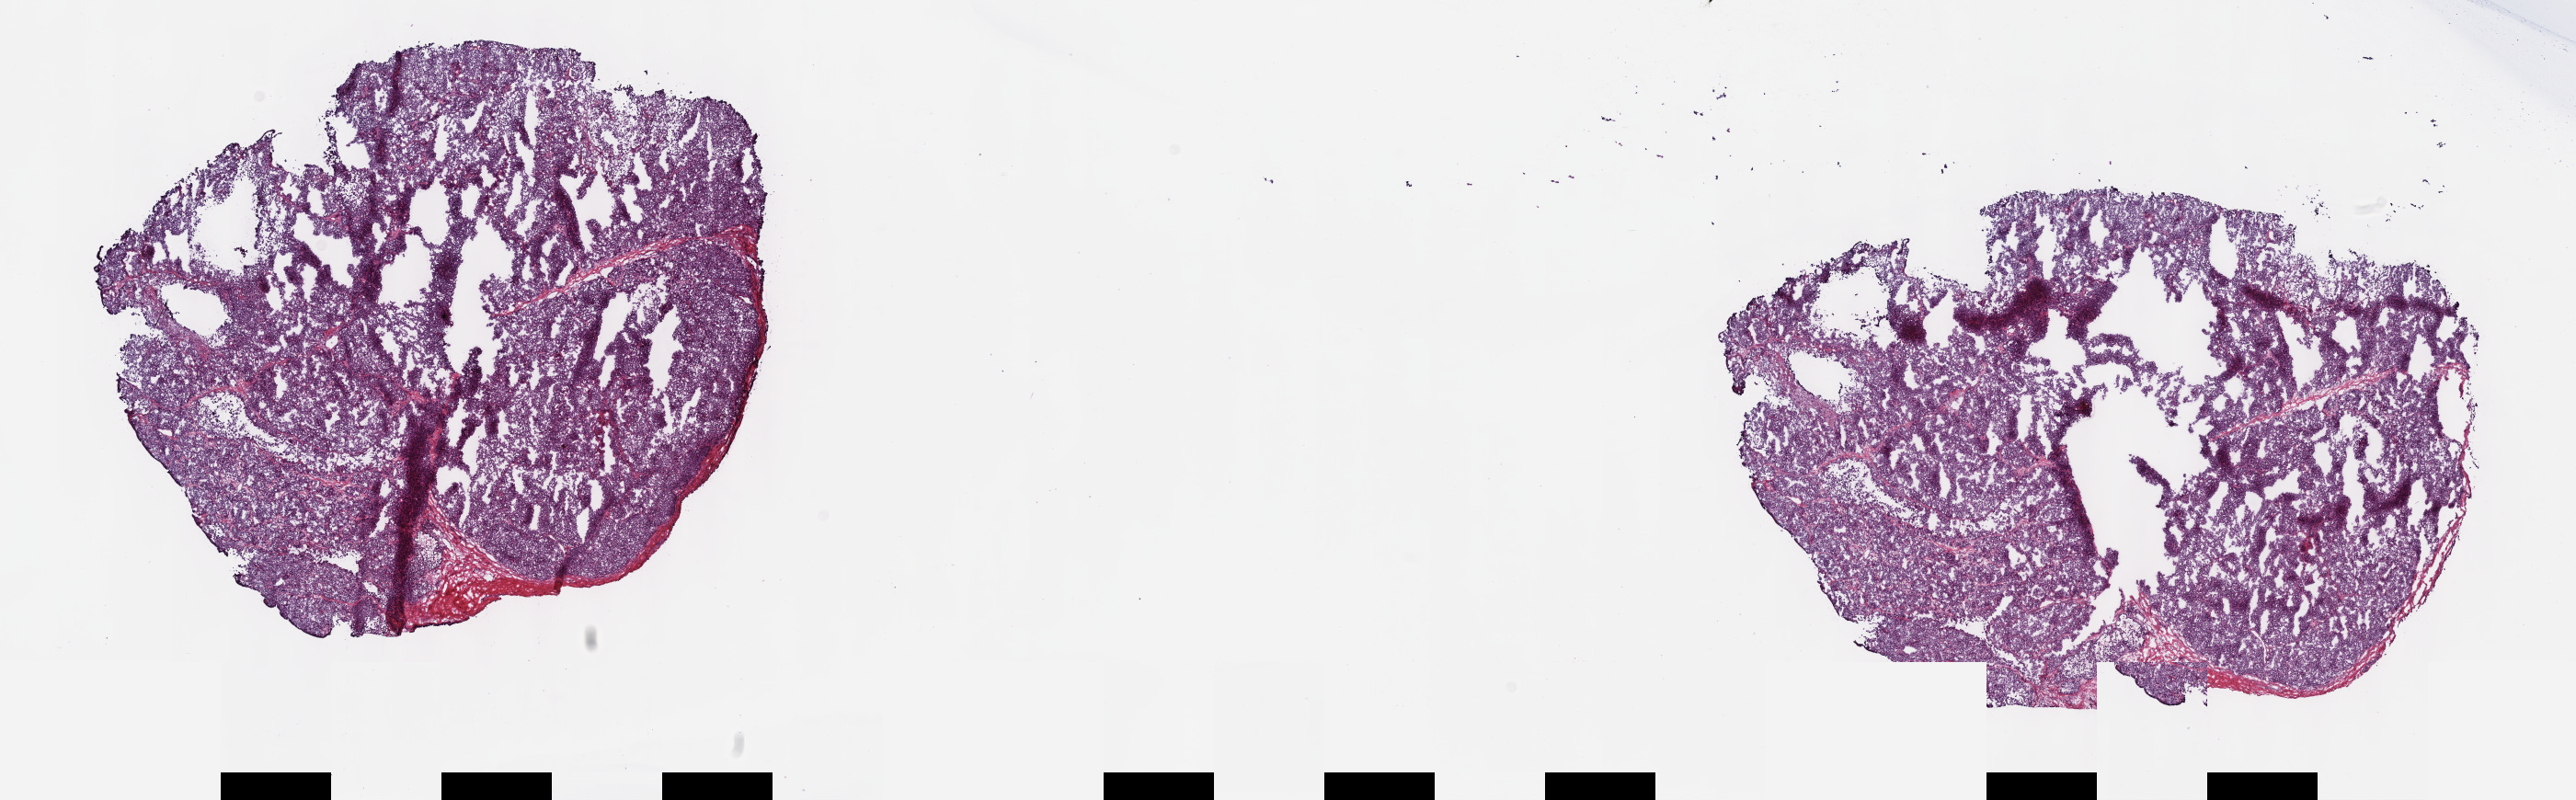
Whole-slide histology image, Hematoxylin and eosin (H&E) stained — whole scanned area (about 22.7 x 7.0 mm, from a 40x scan) shown as a low-resolution overview, frozen section from the top of the tissue portion, metastatic tumour sample, sampled site not recorded. Patient: male, age at initial diagnosis 43 years. Slide review estimates, as recorded: tumour cells 100%, tumour nuclei 97%, normal cells 0%, stromal cells 0%, necrosis 0%. Infiltration values recorded for this section: lymphocyte infiltration 0%, monocyte infiltration 0%, neutrophil infiltration 0%.
- this section: metastatic tumour tissue
- patient diagnosis: Malignant melanoma, NOS